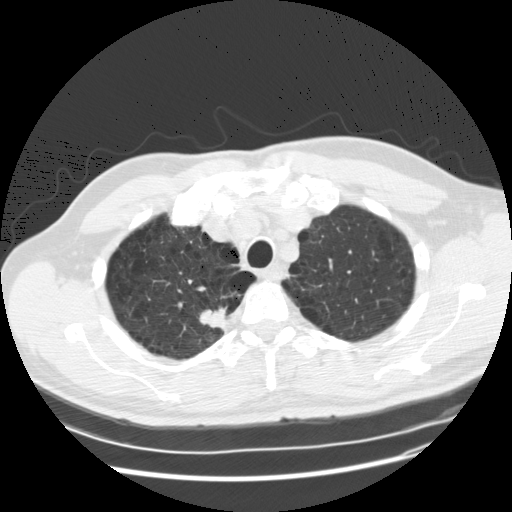
Axial slice from a low-dose chest CT screening exam. First (baseline) screen. Lung window (W 1500 / L -600 HU). 2.5 mm slice thickness. 120 kVp. Slice 24 of 132 in the series. 512 × 512 image matrix, field of view 380 × 380 mm. Male, age 61 years at enrolment. Former smoker at enrolment.
Expert reader's lesion annotation, box from (x=194, y=291) to (x=236, y=341) px. The exam's reader record, not a measurement of the box and not confirmed to be the same lesion: non-calcified nodule or mass ≥4 mm, right upper lobe, 19 × 13 mm, poorly defined margins, soft tissue attenuation. Official screen result: positive, change unspecified: nodule(s) >= 4 mm or enlarging nodule(s), mass(es), or other non-specific abnormalities suspicious for lung cancer. Participant outcome: lung cancer diagnosed 62 days after this screen — squamous cell carcinoma, NOS, right upper lobe, poorly differentiated (G3), stage IA (AJCC 6th edition), 20 mm at pathology.